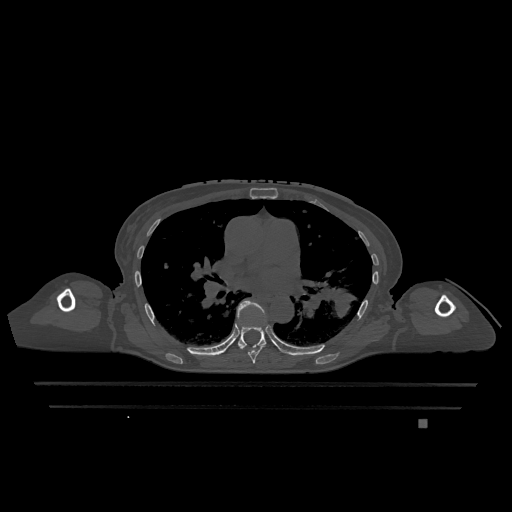
CT including the spine, one axial slice; position 763 of 1317 along the scan axis; bone window (W 1800 / L 400 HU); 0.5 mm slice thickness; 512 × 512 image matrix, field of view 500 × 500 mm. Female patient, age 74 years. From the clinical record (not read from this slice): primary cancer: lung; vertebrae with lytic lesions (as recorded): T1, T4, T5, T6, L4, L5.
Outlined on this slice (semi-automatically segmented with operator editing):
- T6 vertebra: bounding box [x1, y1, x2, y2] px = [239, 345, 264, 364]
- T7 vertebra: [237, 300, 267, 348]